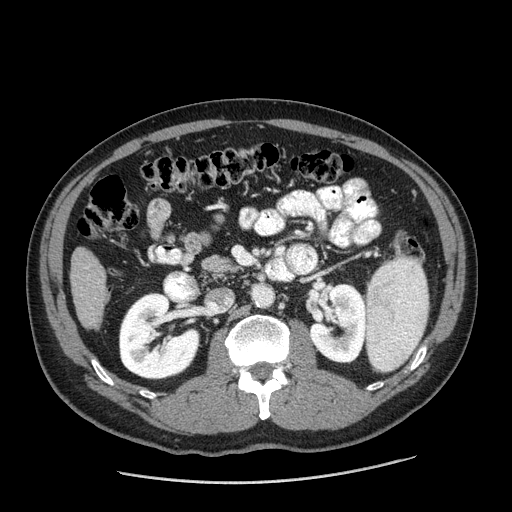
Contrast-enhanced abdominal CT (liver protocol), one axial slice; one of 2 acquisitions stored at this slice position; soft-tissue window (W 400 / L 40 HU); 512 × 512 image matrix, field of view 400 × 400 mm. Case-level facts recorded for this patient, not image findings: diagnosis: hepatocellular carcinoma (patient treated with transarterial chemoembolisation; whether this scan precedes or follows treatment is not stated here); TNM stage (as recorded): Stage-II; Child-Pugh class: A; tumour nodularity: multinodular; tumour size: 2.6 cm.
Outlined on this slice (semi-automatically segmented with operator editing):
- liver parenchyma outside the tumour (the mass and vessels are separate outlines, so this box may not span the whole liver): bounding box [x1, y1, x2, y2] px = [70, 248, 108, 328]